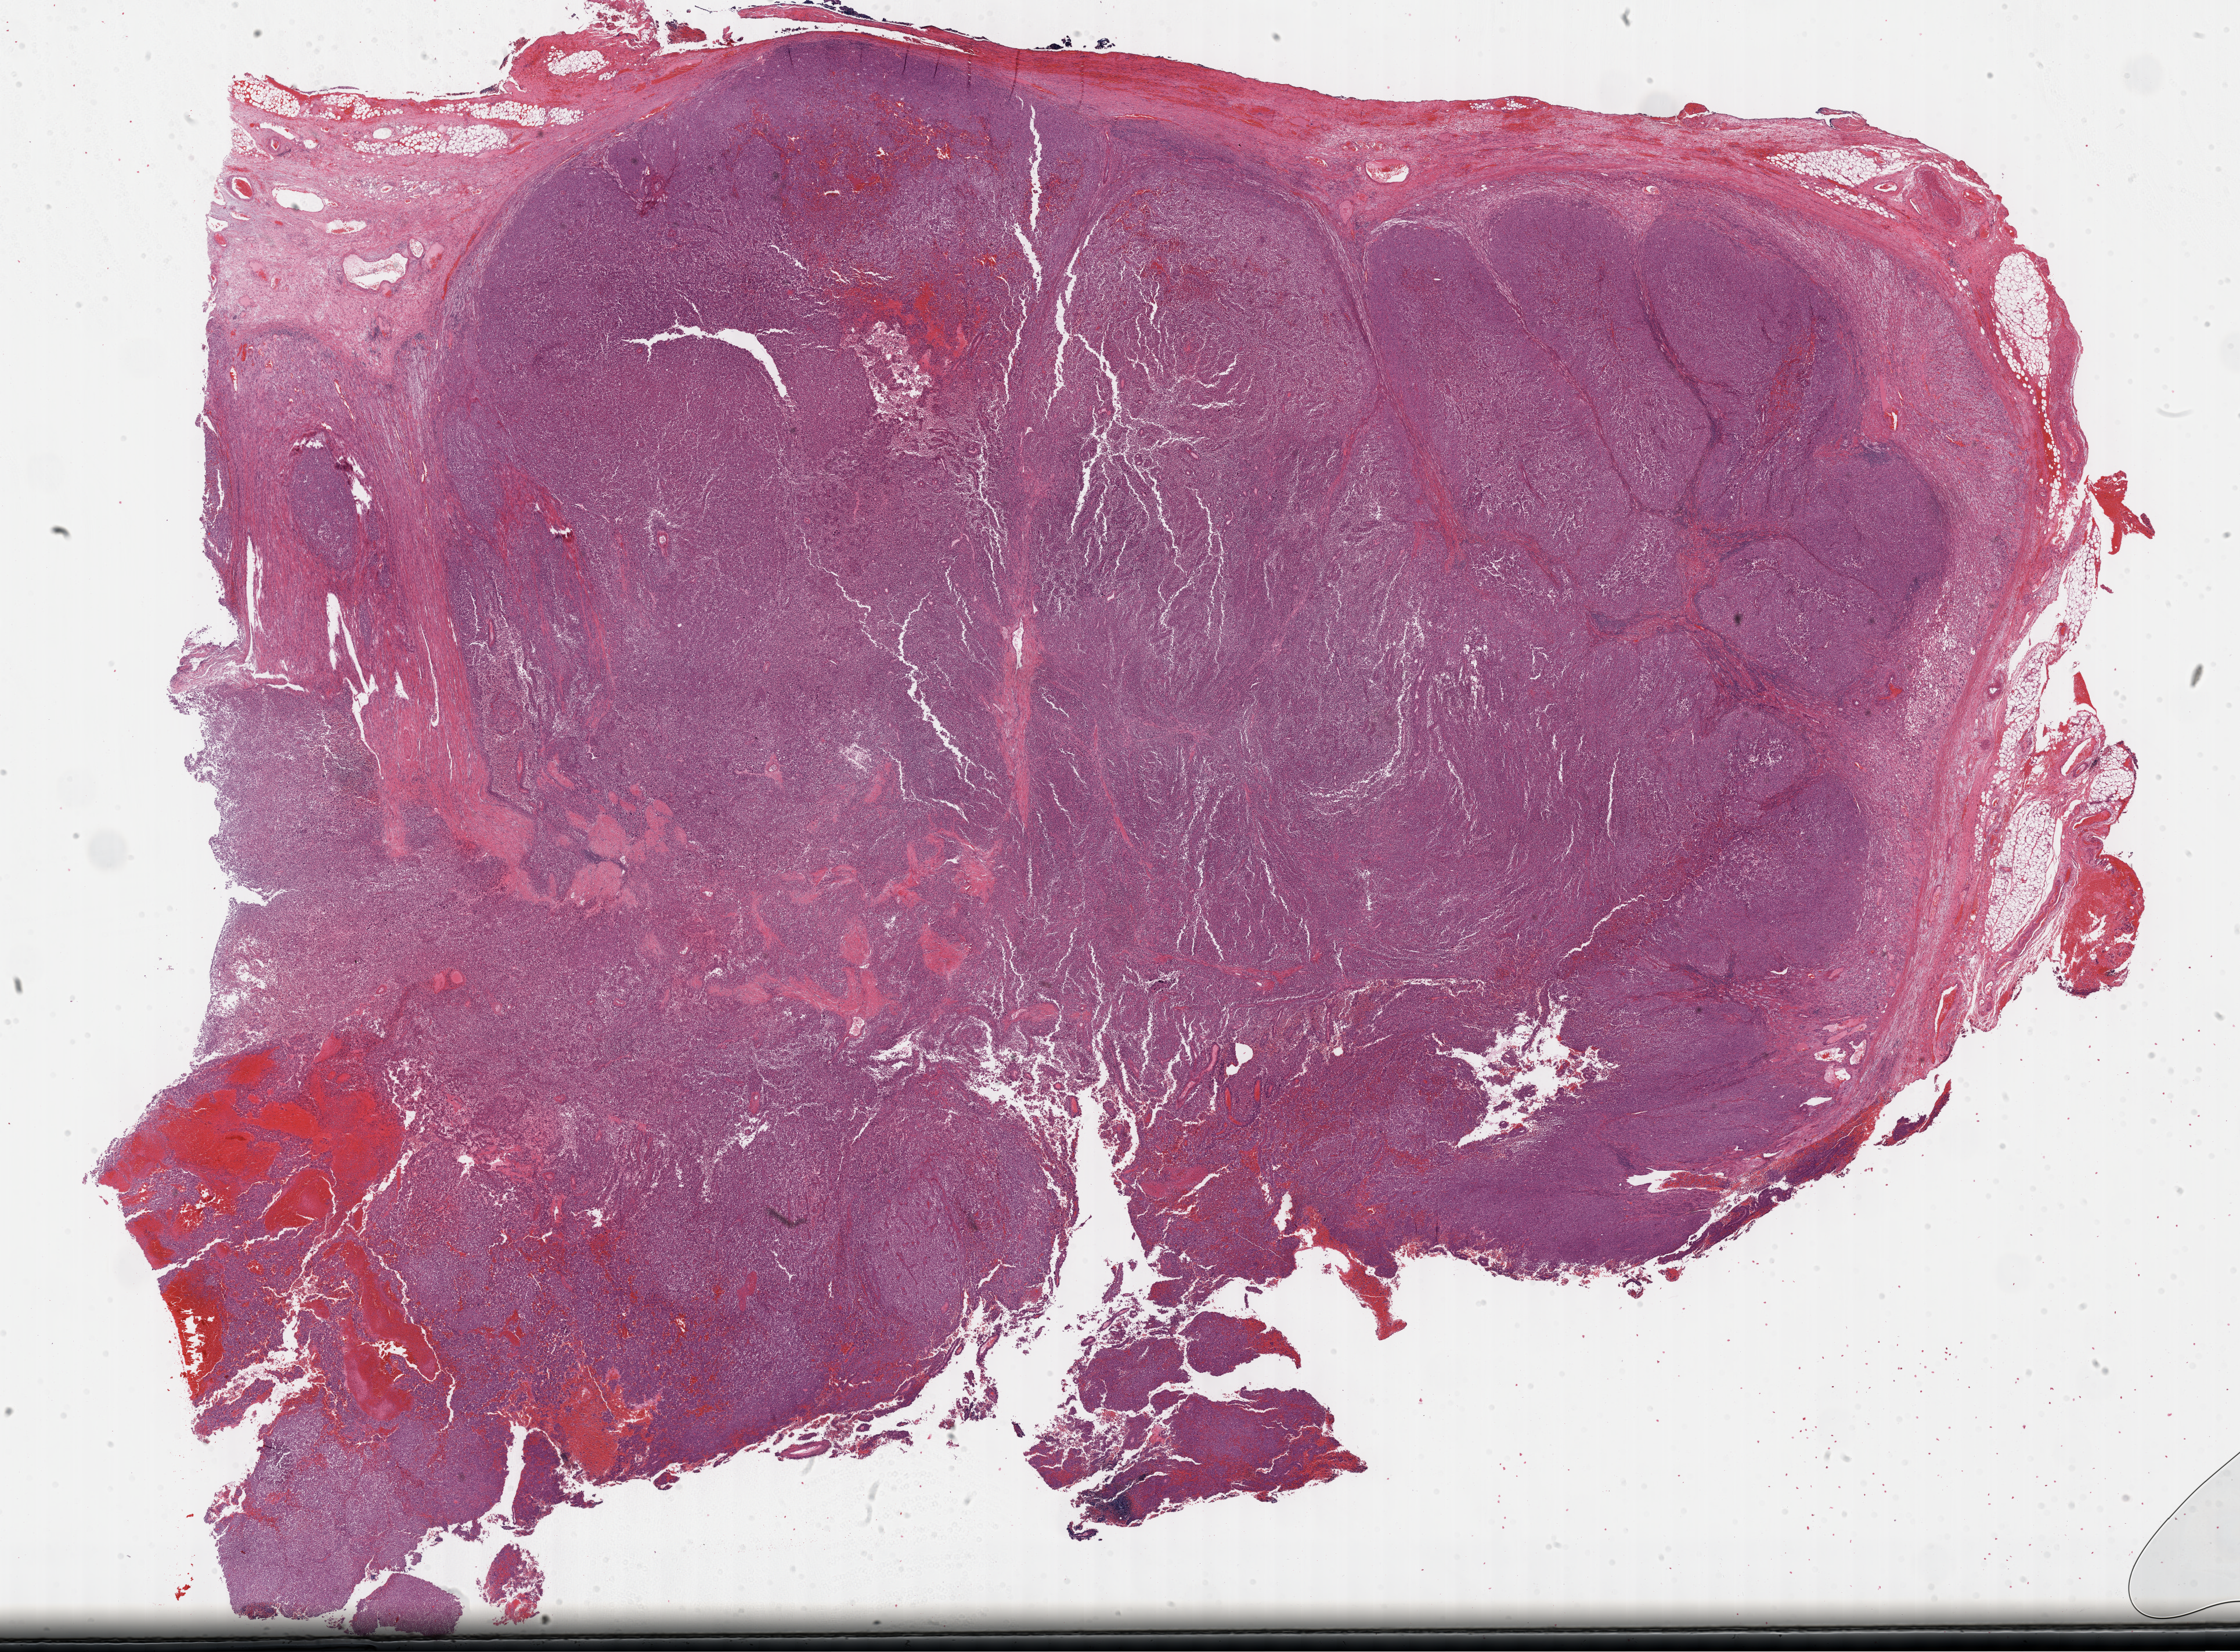
Digitized H&E tissue section (whole slide), whole scanned area (about 31.2 x 23.0 mm) shown as a low-resolution overview. Formalin-fixed paraffin-embedded (FFPE) diagnostic section. Sample: primary tumour, adrenal cortex. Male, age 52 years at initial diagnosis.
Pathologic diagnosis: Adrenal cortical carcinoma (cortex of adrenal gland).